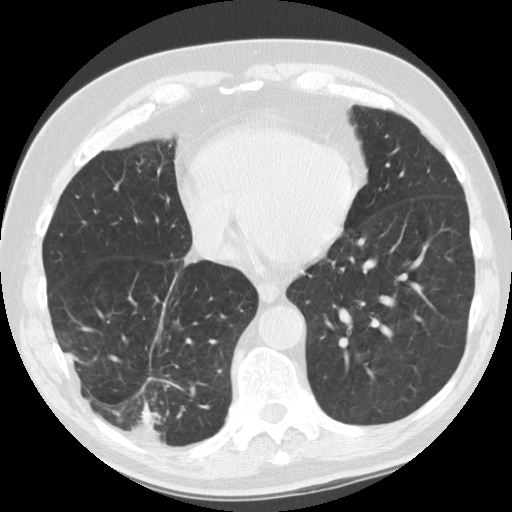
Low-dose screening chest CT, one axial slice; position 38 of 135 along the scan axis; reconstruction kernel STANDARD; lung window (W 1500 / L -600 HU); 512 × 512 image matrix.
Structures marked on this image (expert manual segmentation):
- lesion 1 (tumor, lower lobe of right lung): bounding box [x1, y1, x2, y2] px = [141, 402, 161, 428]